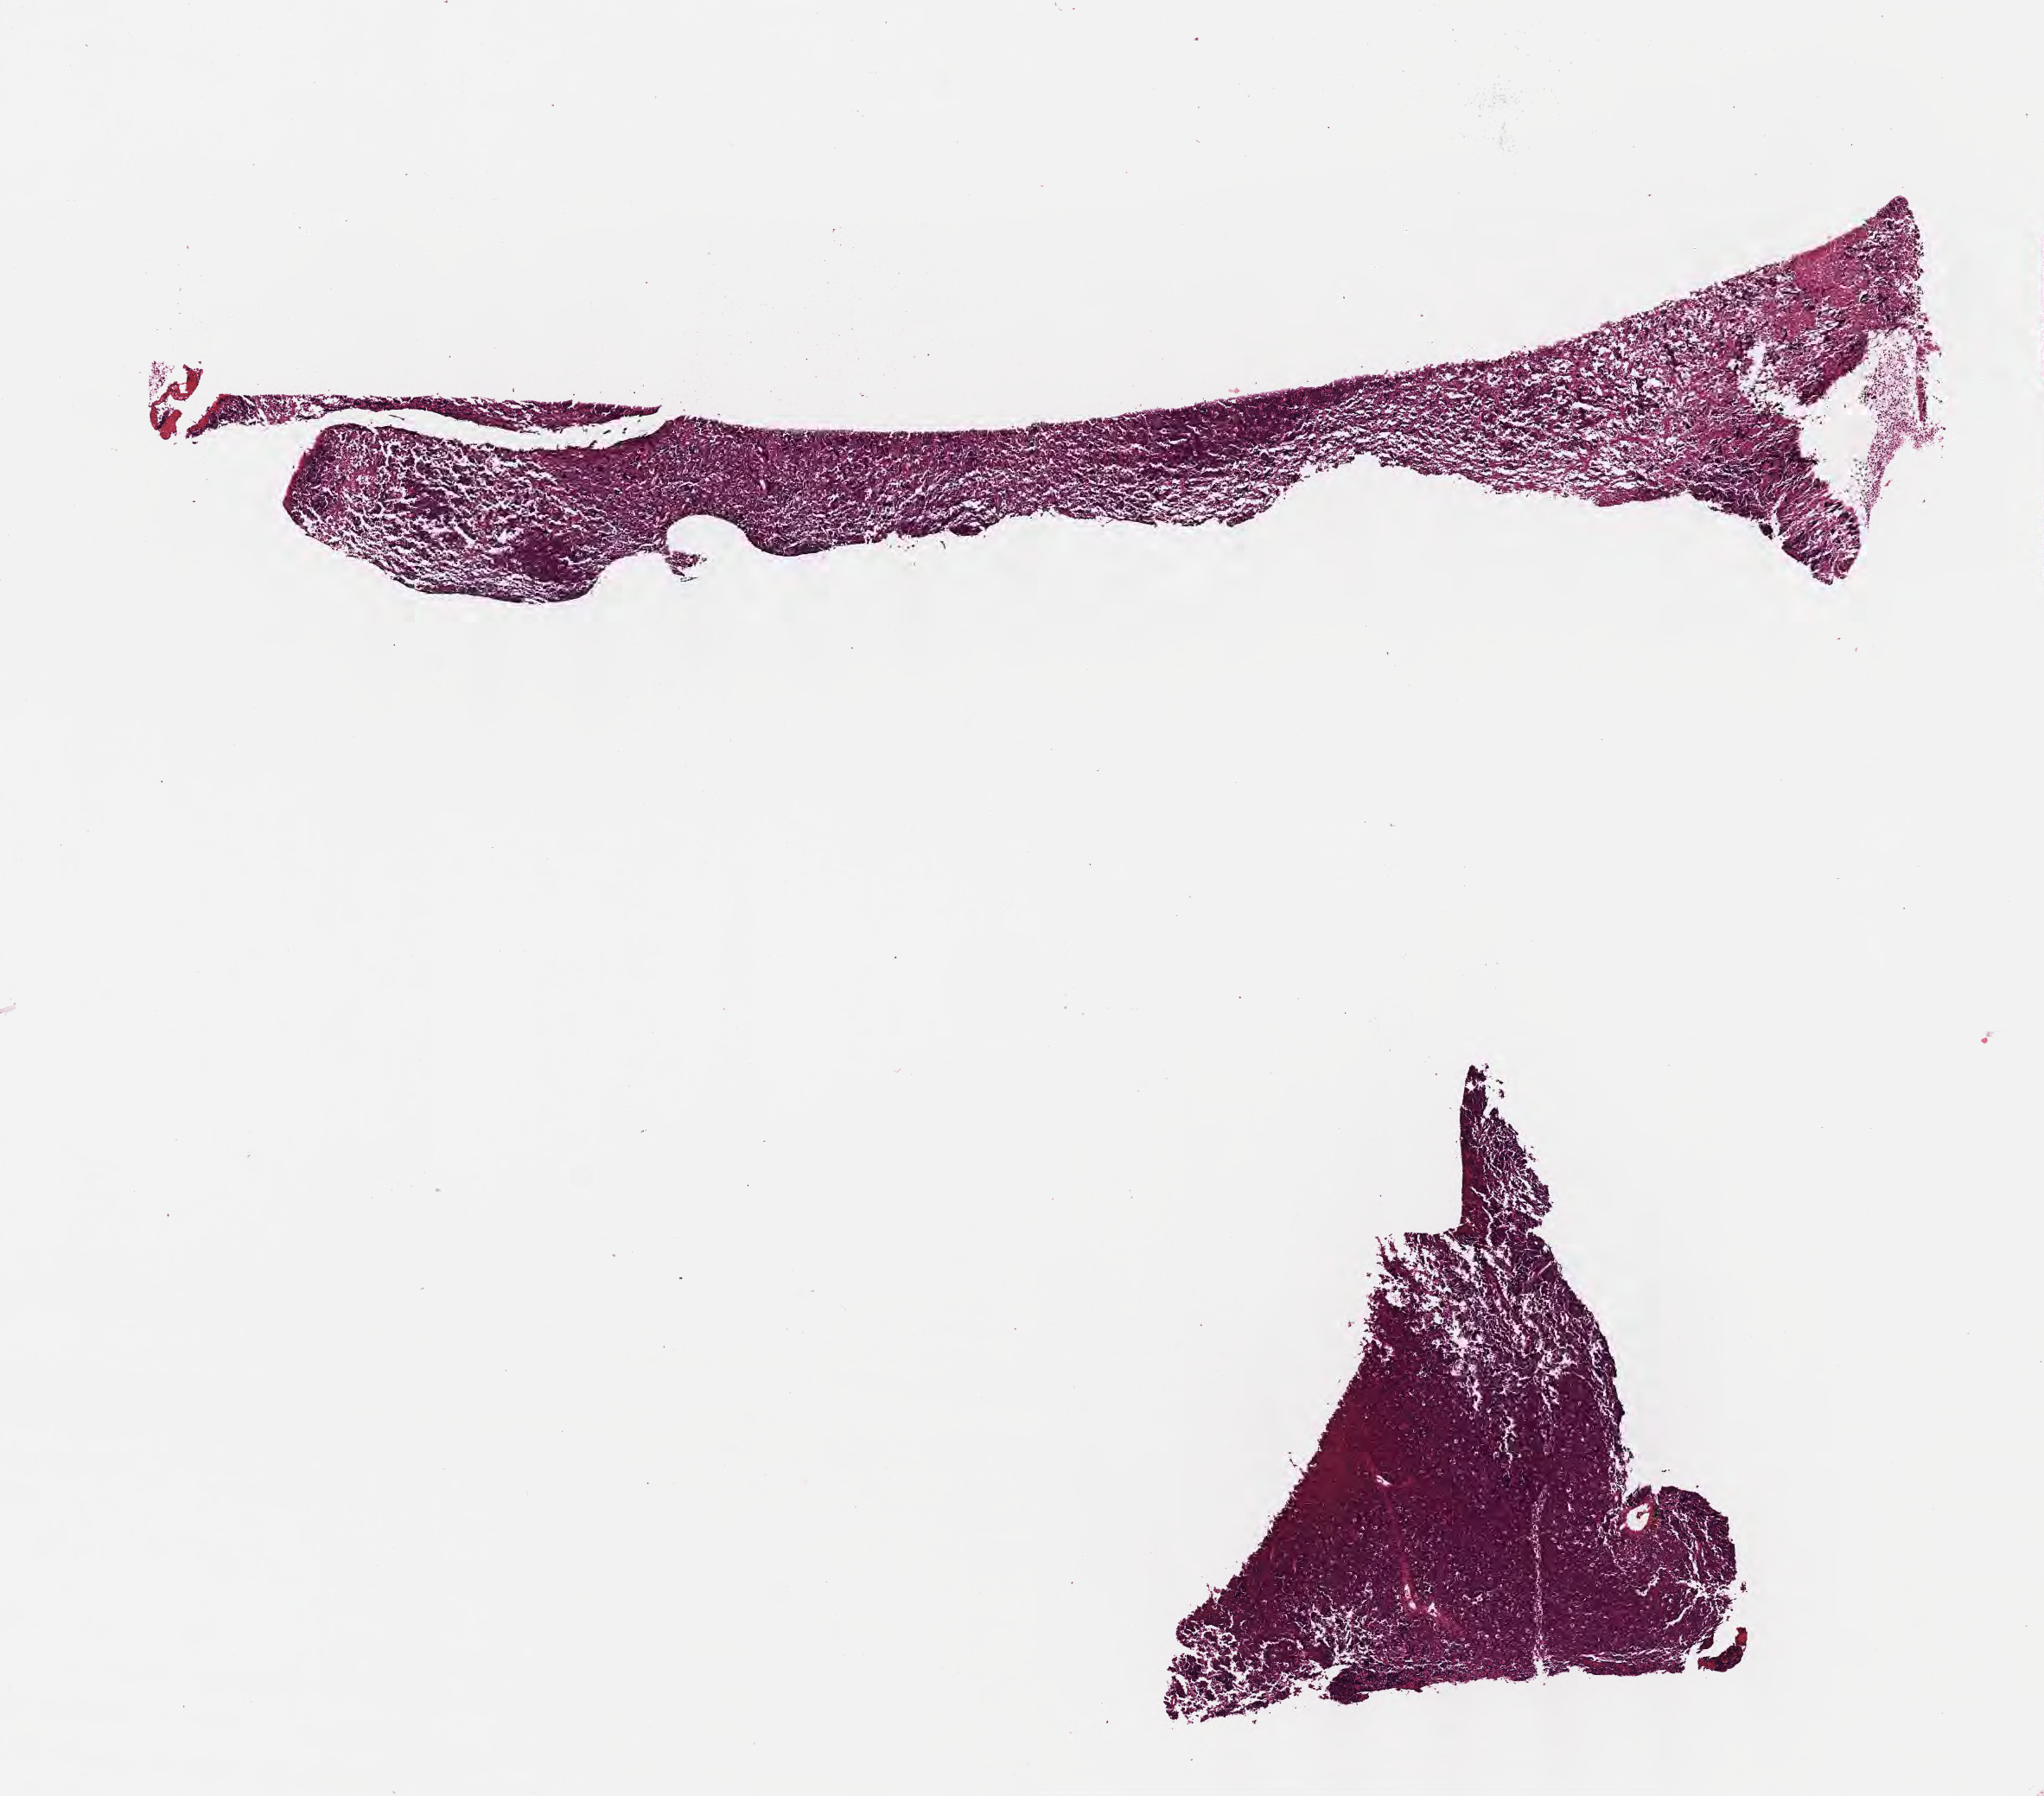
Digitized haematoxylin and eosin-stained section, whole scanned area (about 9.6 x 8.4 mm) shown as a low-resolution overview; formalin-fixed, paraffin-embedded (FFPE) tissue; primary tumor. Patient: male, age at initial diagnosis 2 years. Pathologist review of this section (percent, as recorded): tumor cells 90%, tumor nuclei 95%, stromal cells 5%, necrosis 5%, normal cells 0%. Inflammatory infiltration, as recorded: lymphocyte infiltration 80%, monocyte infiltration 10%, neutrophil infiltration 0%.
Diagnosis: Burkitt lymphoma, NOS. Ann Arbor stage (patient): Stage III. Section: top of the tissue portion.